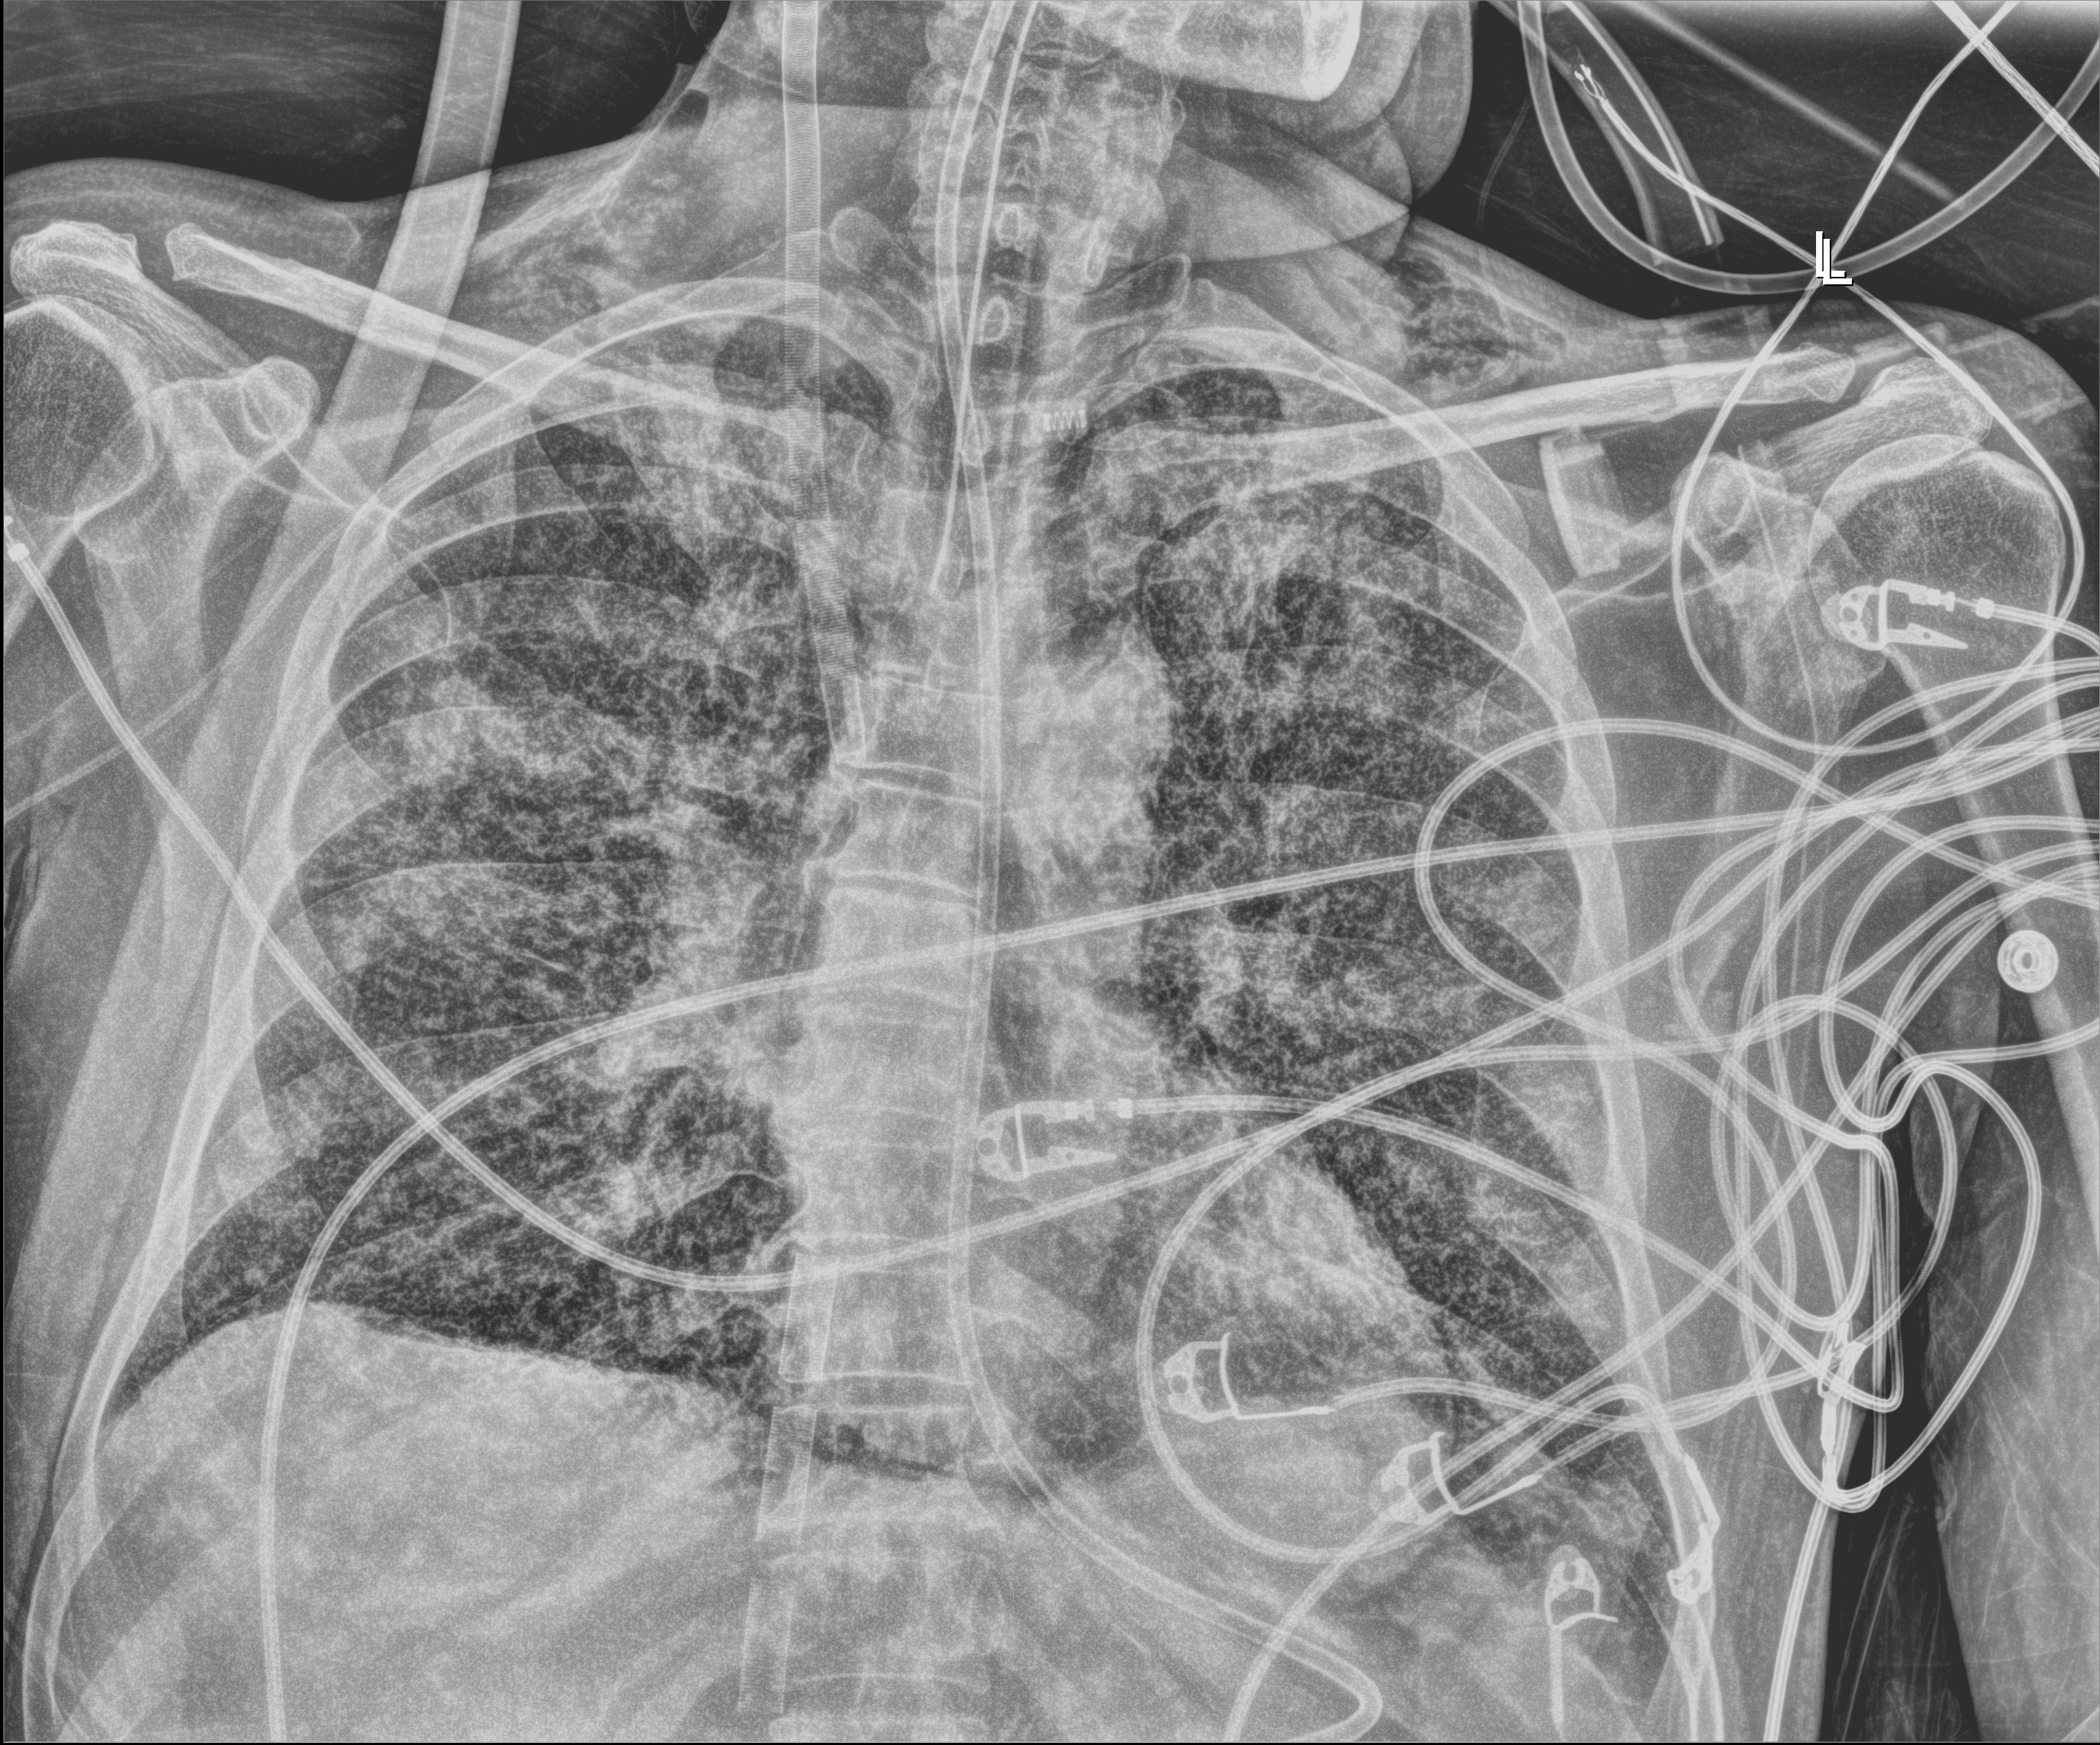
Chest radiograph (digital radiography), anteroposterior (AP) projection. Male patient hospitalised with COVID-19, age 18–59 years.
Hospital-stay facts (about this admission, not read from this image; timing relative to this image not recorded):
- chronic kidney disease (admission record): no
- mechanically ventilated during this hospital stay: yes